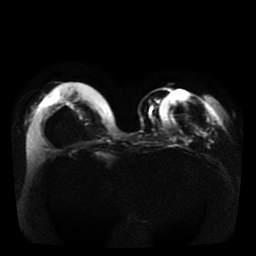
Breast MRI, one axial slice; position 13 of 41 along the scan axis; diffusion-weighted series; image 2 of 4 stored at this slice position (different b-values; order by instance number); 1.5 T; 256 × 256 image matrix, field of view 330 × 330 mm. Female patient.
Annotated regions visible in this slice (expert manual segmentation):
- tumour on diffusion-weighted imaging: bounding box [x1, y1, x2, y2] px = [200, 130, 204, 136]